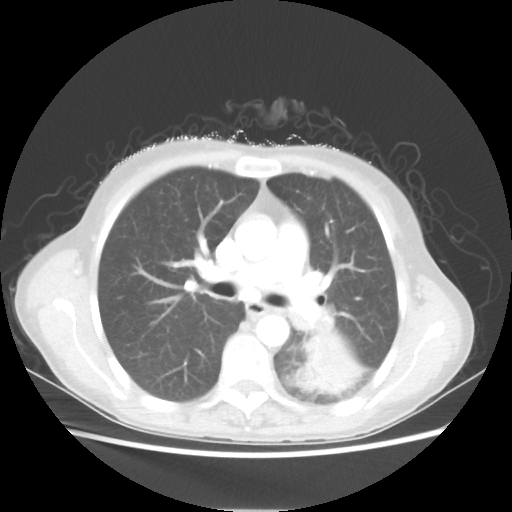
Chest CT, one axial slice. Position 34 of 56 along the scan axis. Lung window (W 1500 / L -600 HU). 5 mm slice thickness. 512 × 512 image matrix. Female patient, age 53 years. Case-level facts recorded for this patient, not image findings: clinical TNM (as recorded): T3 N0 M0.
Outlined on this slice (rectangle marked by the reading radiologist):
- lung tumour (recorded histology: adenocarcinoma): bounding box [x1, y1, x2, y2] px = [298, 333, 363, 395]